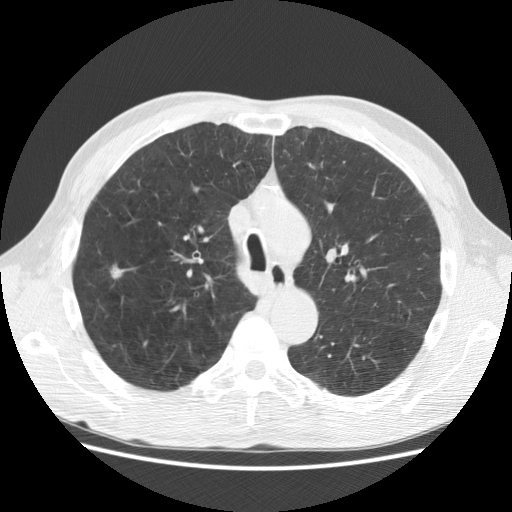
Low-dose screening chest CT, one axial slice. Slice 204 of 282 in the series (ordered by position). Reconstruction kernel STANDARD. 120 kVp. Lung window (W 1500 / L -600 HU). 2.5 mm slice thickness. 512 × 512 image matrix, field of view 367 × 367 mm.
Structures marked on this image (outlined manually by an expert reader):
- lesion 1 (tumor, upper lobe of right lung): bounding box (x1, y1, x2, y2) in pixels: (112, 268, 124, 278)